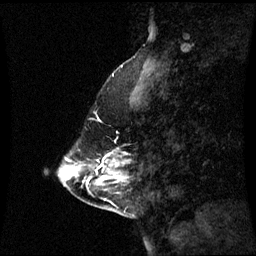
Breast MRI (dynamic contrast-enhanced), one sagittal slice; slice 19 of 60 in the series (ordered by position); dynamic contrast-enhanced series, image 2 of 3 at this slice position (ordered by acquisition); 1.5 T; TE 4.2 ms, TR 8.9 ms; 256 × 256 image matrix. Female patient, age 43 years. From the clinical record (not read from this slice): setting: breast cancer imaged before/during neoadjuvant chemotherapy; receptor status: HR-positive, HER2-negative.
Outlined on this slice (semi-automatic segmentation, software-assisted and operator-edited):
- analysis volume of interest (the breast-tissue region the enhancement analysis was run in; not a lesion): box from (x=78, y=152) to (x=128, y=193) px
- tumour enhancement mask (voxels above the 70 % enhancement threshold inside the analysis volume of interest): (x=98, y=160)–(x=103, y=173)